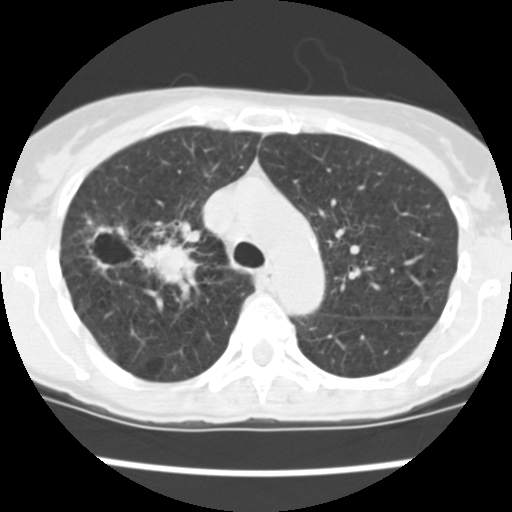
Low-dose screening chest CT, one axial slice. Slice 175 of 252 in the series (ordered by position). Reconstruction kernel STANDARD. 120 kVp. Lung window (W 1500 / L -600 HU). 512 × 512 image matrix, field of view 276 × 276 mm.
Structures marked on this image (manually delineated by an expert):
- lesion 2 (tumor, lower lobe of right lung): bounding box [x1, y1, x2, y2] px = [94, 222, 199, 289]